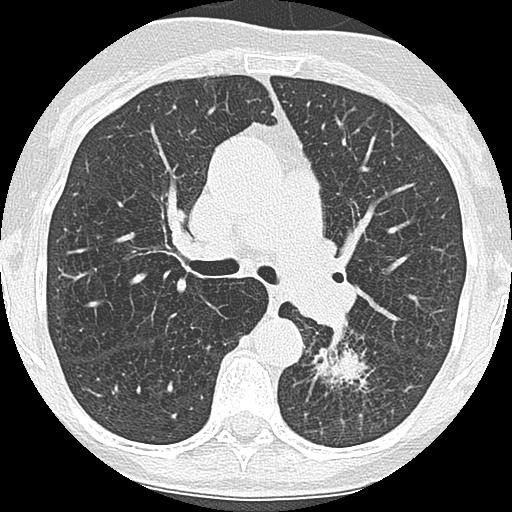
Low-dose screening chest CT, one axial slice. Slice 110 of 171 in the series (ordered by position). Reconstruction kernel LUNG. 120 kVp. Lung window (W 1500 / L -600 HU). 2.5 mm slice thickness. 512 × 512 image matrix.
Outlined on this slice (outlined manually by an expert reader):
- lesion 1 (tumor, lower lobe of left lung): bounding box [x1, y1, x2, y2] px = [313, 344, 368, 385]